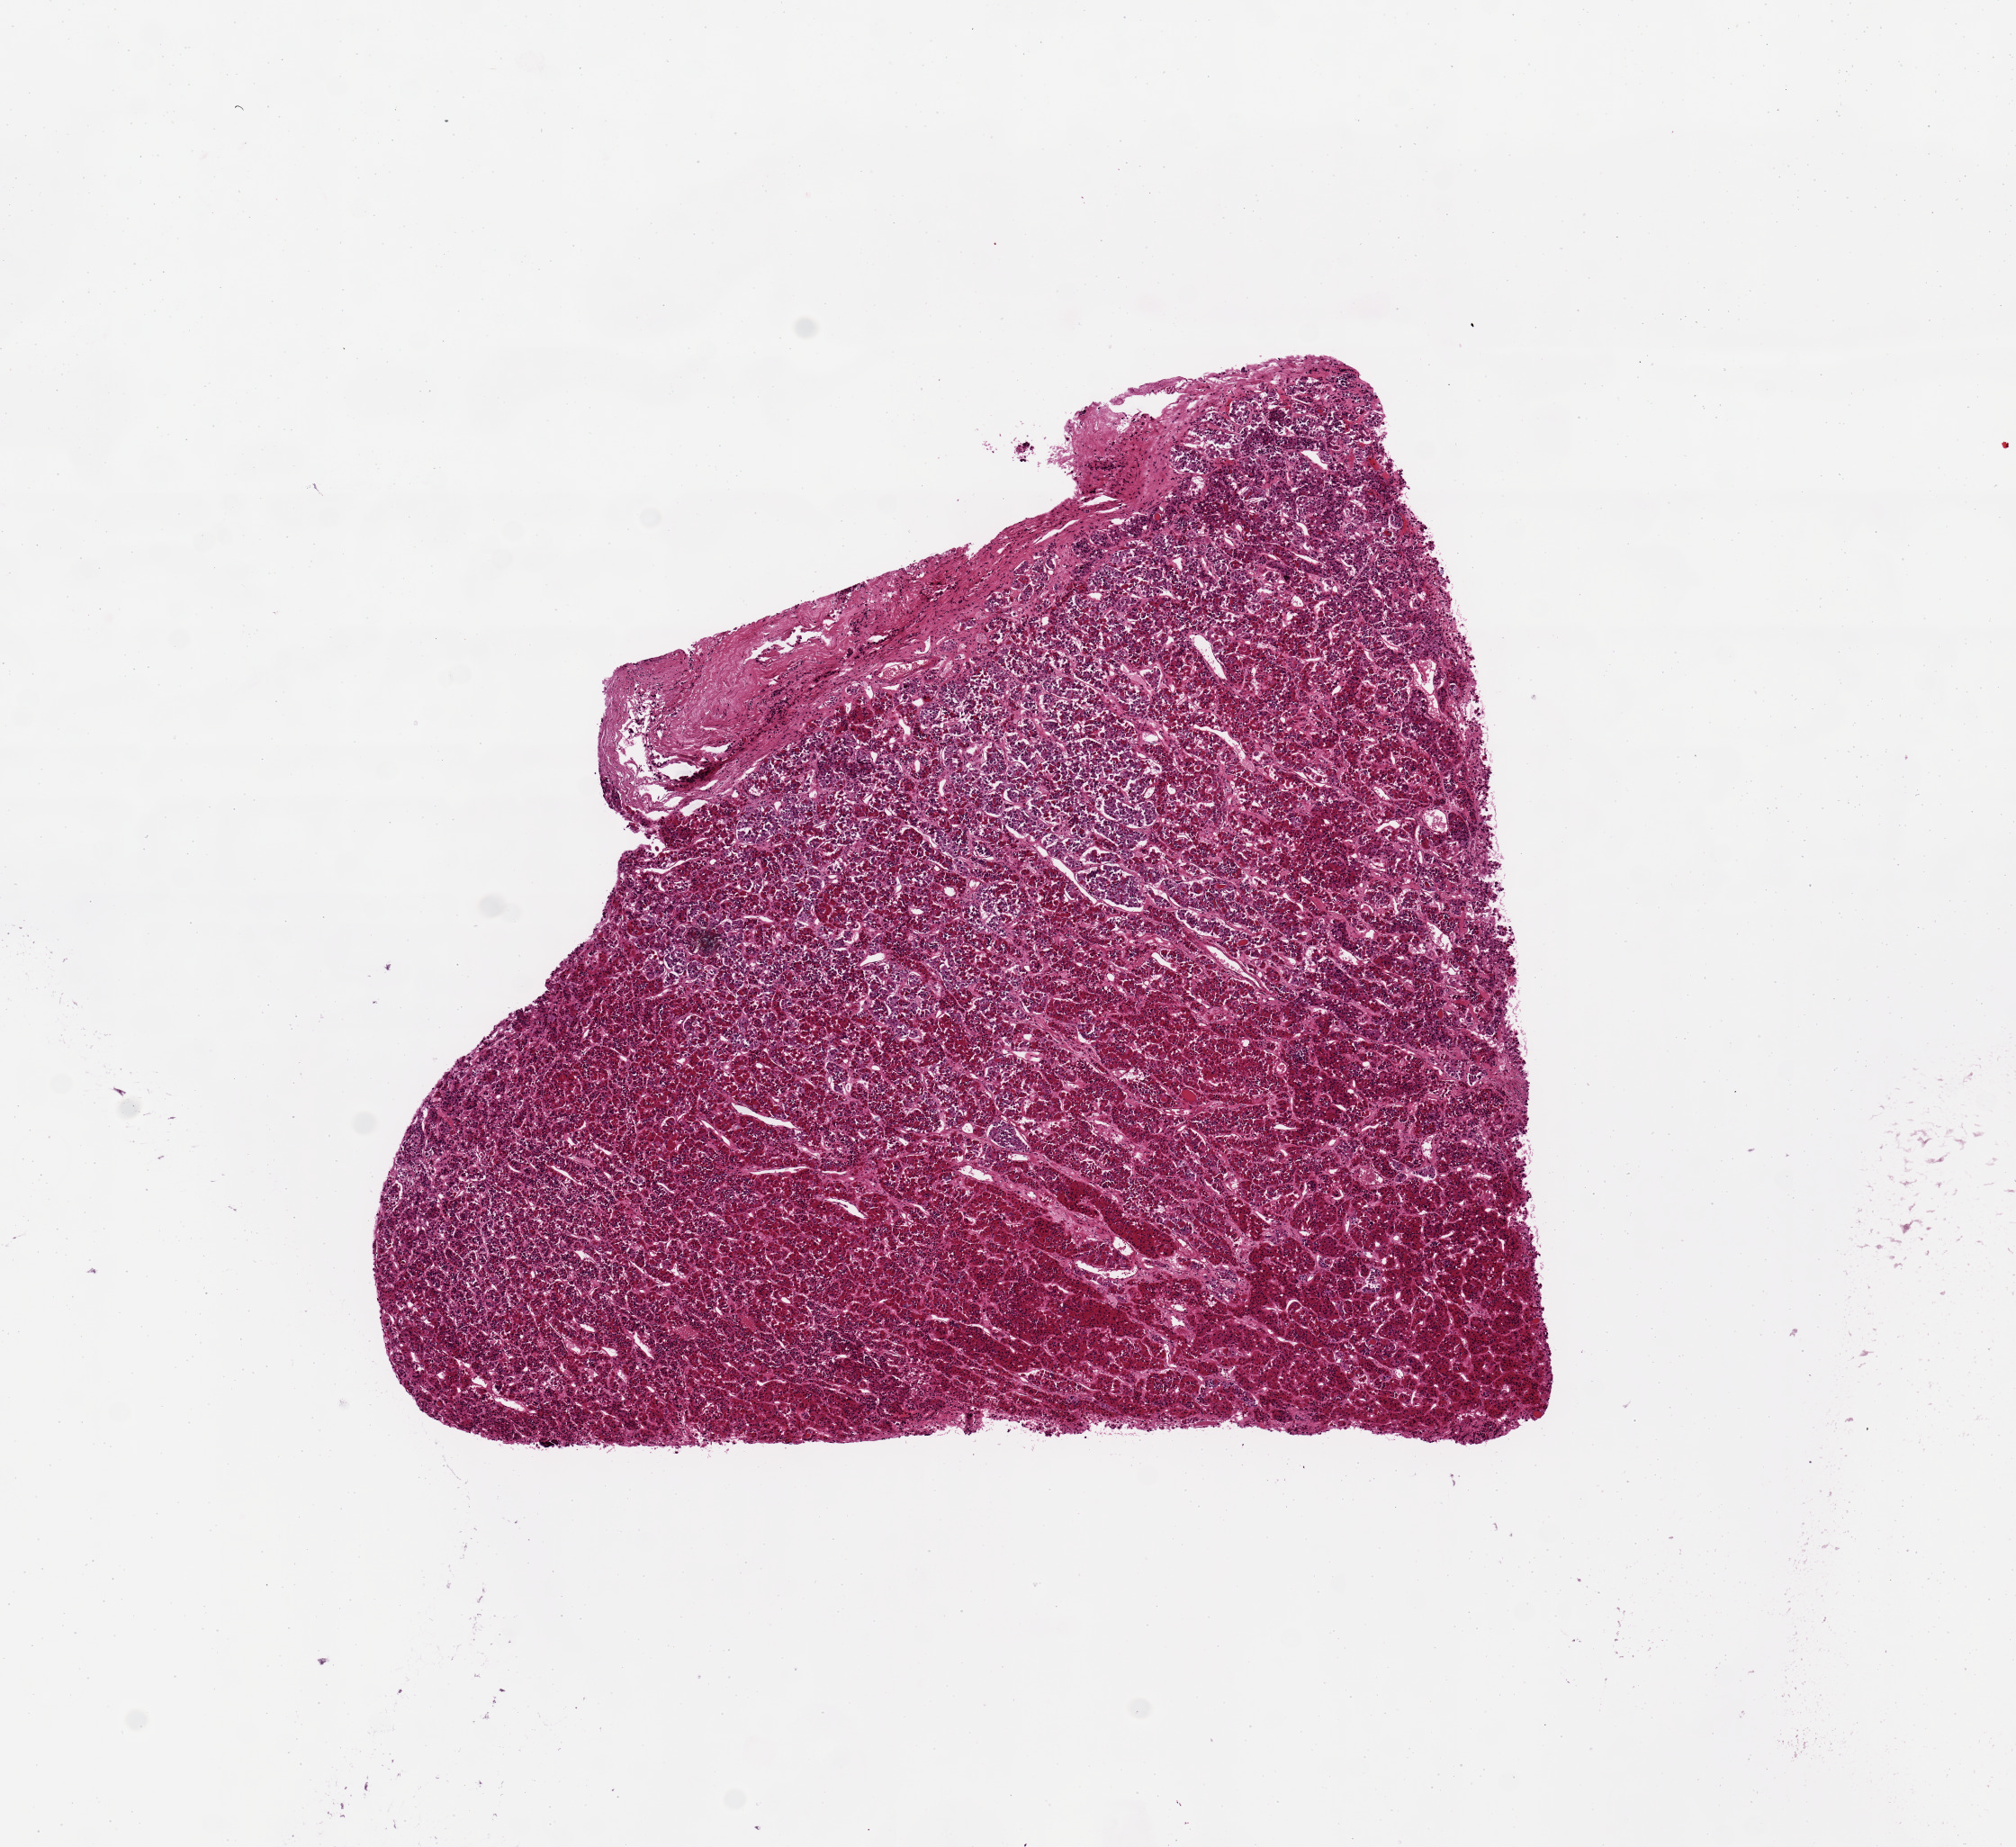
Whole-slide image, H&E stain, whole scanned area (about 8.9 x 8.1 mm) shown as a low-resolution overview; PAXgene-fixed, paraffin-embedded tissue; target tissue: pituitary; tissue donor sample. Donor: female.
Pathologist's review note for this sample: Moderately autolyzed.